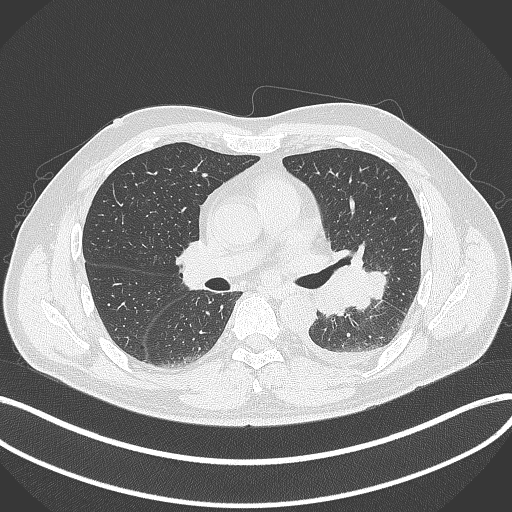
Chest CT, one axial slice. Position 200 of 342 along the scan axis. Reconstruction kernel B70f. 120 kVp. Lung window (W 1500 / L -600 HU). 1 mm slice thickness. 512 × 512 image matrix, field of view 400 × 400 mm. Patient: male, 58 years. Case-level facts recorded for this patient, not image findings: clinical TNM (as recorded): T3 N1 M1b; histopathological grade: G3.
Structures marked on this image (rectangle marked by the reading radiologist):
- lung tumour (recorded histology: small cell carcinoma): bounding box <334,252,389,312> (left, top, right, bottom; pixels)